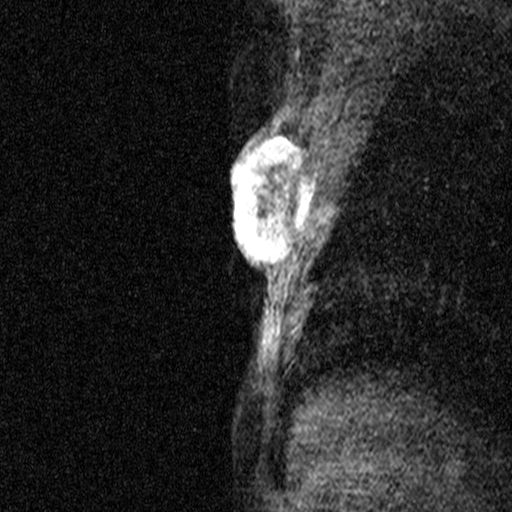
Breast MRI (dynamic contrast-enhanced), one sagittal slice; position 30 of 44 along the scan axis; dynamic contrast-enhanced study with each time point stored as its own series, time point 2 of 3 at this slice position (early post-contrast, ordered by acquisition time); 1.5 T; TE 4.5 ms, TR 11 ms; 3 mm slice thickness; 512 × 512 image matrix, field of view 200 × 200 mm. Female patient, age 44 years. Case-level facts recorded for this patient, not image findings: setting: breast cancer imaged before/during neoadjuvant chemotherapy; receptor status: HR-positive, HER2-negative.
Structures marked on this image (semi-automatic segmentation, software-assisted and operator-edited):
- analysis volume of interest (the breast-tissue region the enhancement analysis was run in; not a lesion): box from (x=218, y=118) to (x=310, y=291) px
- tumour enhancement mask (voxels above the 90 % enhancement threshold inside the analysis volume of interest): (x=230, y=133)–(x=310, y=257)